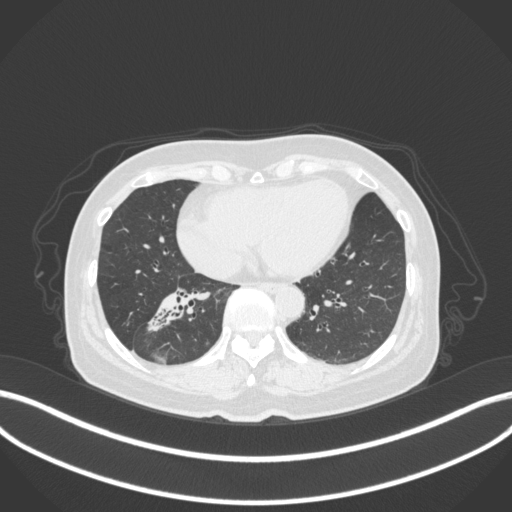
Chest CT, one axial slice. Reconstruction kernel B31f. Lung window (W 1500 / L -600 HU). 1 mm slice thickness. 512 × 512 image matrix, field of view 400 × 400 mm. Female patient, age 67 years. Case-level facts recorded for this patient, not image findings: clinical TNM (as recorded): T1c N1 M0.
Outlined on this slice (bounding box drawn by a radiologist):
- lung tumour (recorded histology: adenocarcinoma): bounding box [x1, y1, x2, y2] px = [146, 278, 213, 335]